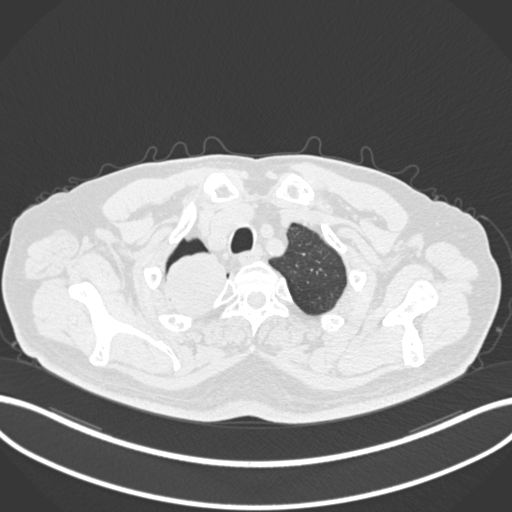
Chest CT, one axial slice; 120 kVp; lung window (W 1500 / L -600 HU); 1 mm slice thickness; 512 × 512 image matrix. Male patient, age 68 years. From the clinical record (not read from this slice): clinical TNM (as recorded): T2a N0 M0.
Outlined on this slice (bounding box drawn by a radiologist):
- lung tumour (recorded histology: adenocarcinoma): bounding box <162,248,237,321> (left, top, right, bottom; pixels)